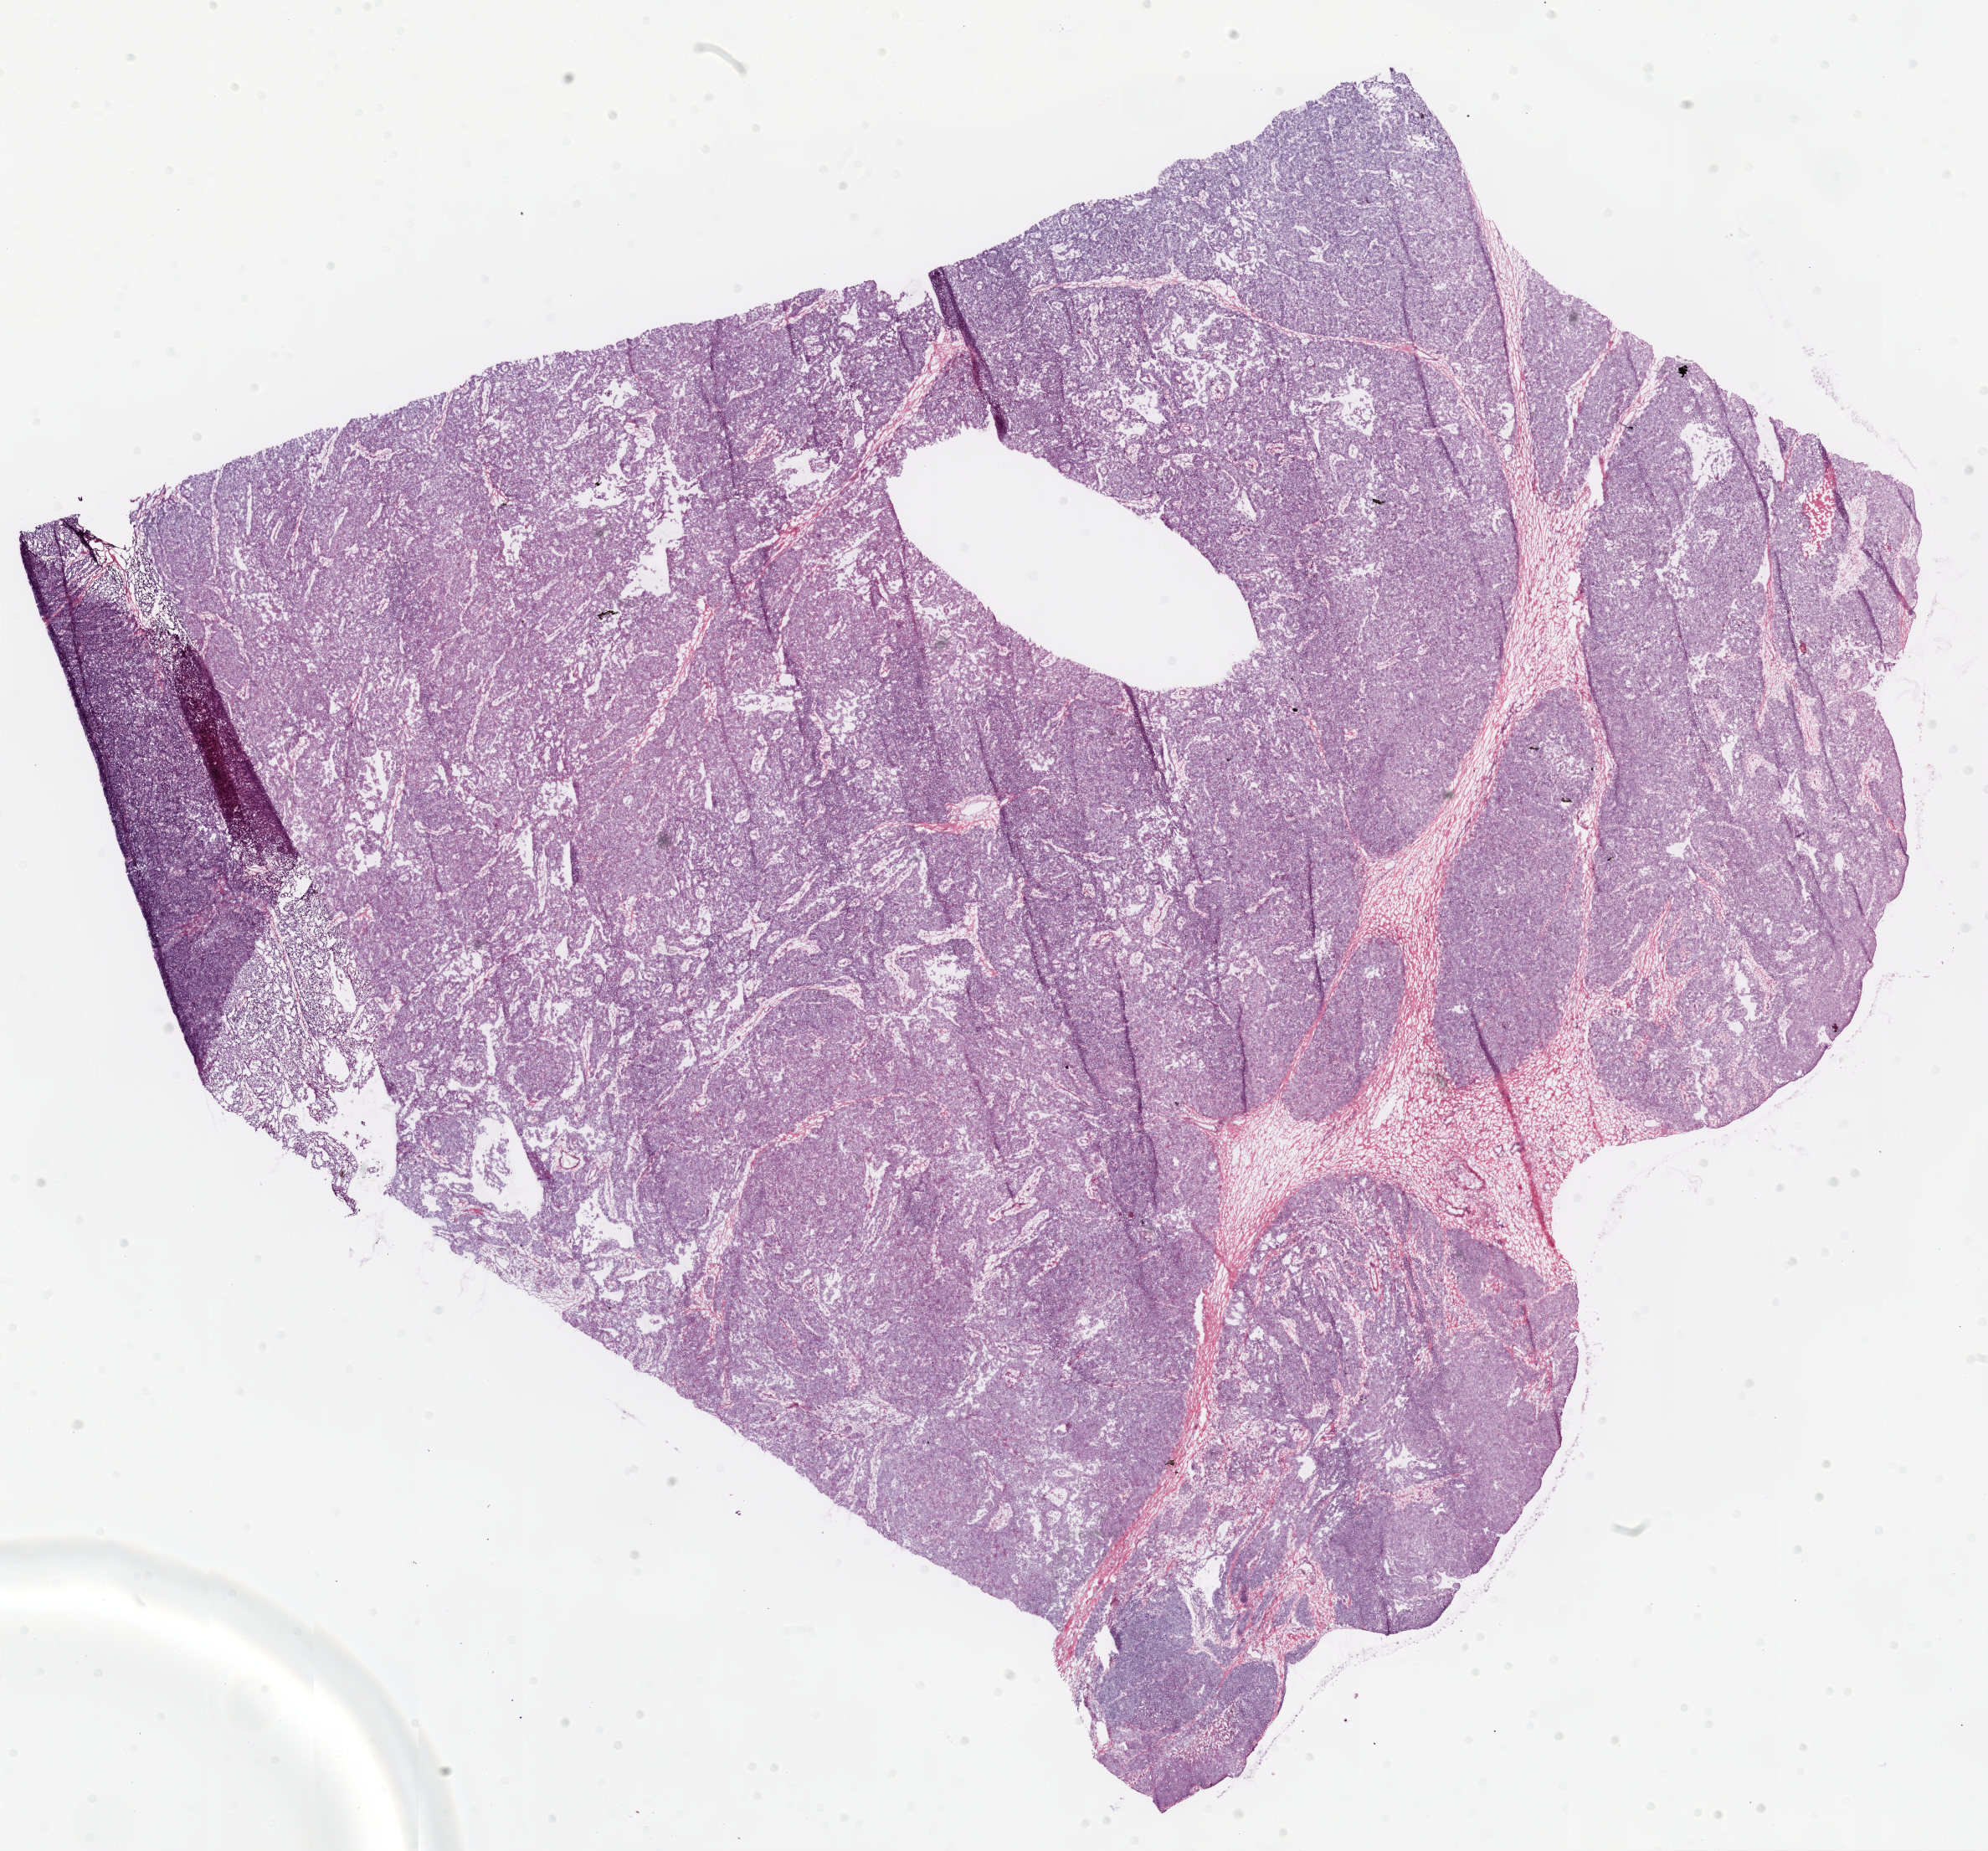
H&E whole-slide image — a low-resolution overview of the entire scanned area, about 19.1 x 17.7 mm (acquisition: 20x scan). Frozen section. Primary tumour sample from the ovary. Female, age 43 years at initial diagnosis. Histologic grade: G3 (poorly differentiated). Composition of this section per pathologist review: tumour cells 74%, tumour nuclei 75%, normal cells 8%, stromal cells 8%, necrosis 10%.
* pathologic diagnosis: Serous cystadenocarcinoma, NOS
* FIGO stage: IIIC